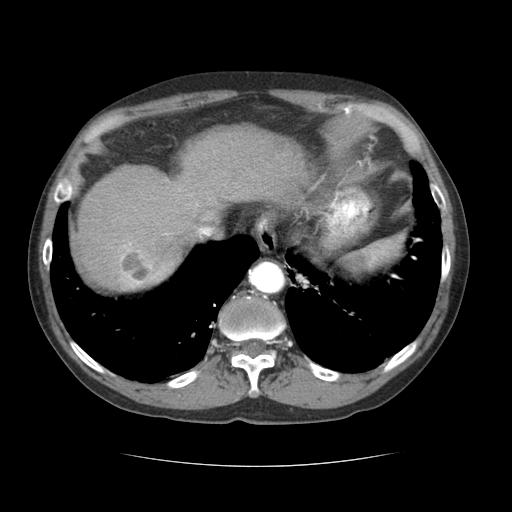
Contrast-enhanced abdominal CT (liver protocol), one axial slice; position 55 of 69 along the scan axis; reconstruction kernel STANDARD; soft-tissue window (W 400 / L 40 HU); 2.5 mm slice thickness; 512 × 512 image matrix. From the clinical record (not read from this slice): diagnosis: hepatocellular carcinoma (patient treated with transarterial chemoembolisation; whether this scan precedes or follows treatment is not stated here); TNM stage (as recorded): Stage-II; Child-Pugh class: B; tumour differentiation: poorly differentiated; tumour nodularity: multinodular.
Structures marked on this image (semi-automatically segmented with operator editing):
- abdominal aorta: bounding box [x1, y1, x2, y2] px = [250, 262, 283, 294]
- liver parenchyma outside the tumour (the mass and vessels are separate outlines, so this box may not span the whole liver): [72, 126, 312, 290]
- mass: [117, 246, 171, 289]
- liver vessels: [124, 242, 132, 247]